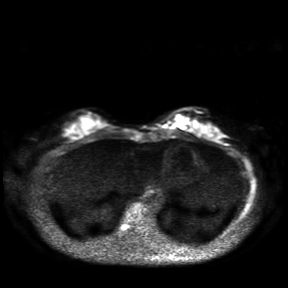
Breast MRI, one axial slice. Position 7 of 30 along the scan axis. Diffusion-weighted series; image 2 of 4 stored at this slice position (different b-values; order by instance number). 3 T. 4 mm slice thickness. 288 × 288 image matrix. Female patient.
Structures marked on this image (expert manual segmentation):
- tumour on diffusion-weighted imaging: box from (x=175, y=116) to (x=183, y=122) px